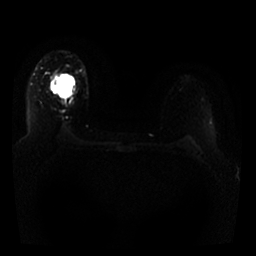
Breast MRI, one axial slice; slice 21 of 25 in the series (ordered by position); diffusion-weighted series; image 2 of 4 stored at this slice position (different b-values; order by instance number); 1.5 T; 4 mm slice thickness; 256 × 256 image matrix, field of view 330 × 330 mm. Female patient.
Annotated regions visible in this slice (manually delineated by an expert):
- tumour on diffusion-weighted imaging: bounding box <57,74,61,96> (left, top, right, bottom; pixels)